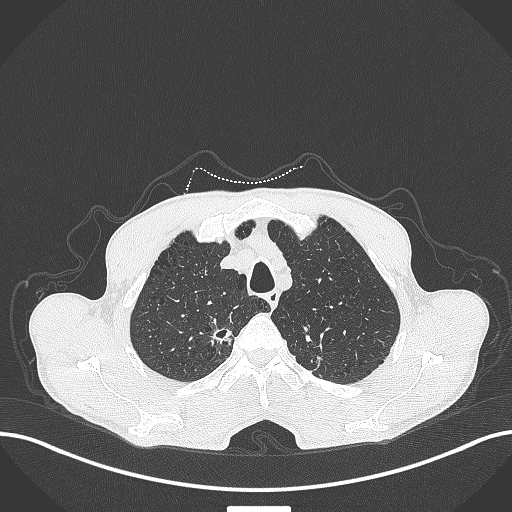
Chest CT, one axial slice. Slice 359 of 445 in the series (ordered by position). Reconstruction kernel B70f. 120 kVp. Lung window (W 1500 / L -600 HU). 1 mm slice thickness. 512 × 512 image matrix, field of view 400 × 400 mm. Patient: male, 70 years. Case-level facts recorded for this patient, not image findings: clinical TNM (as recorded): T1a N0 M0; histopathological grade: G1-2.
Outlined on this slice (bounding box drawn by a radiologist):
- lung tumour (recorded histology: adenocarcinoma): bounding box (x1, y1, x2, y2) in pixels: (207, 322, 234, 348)